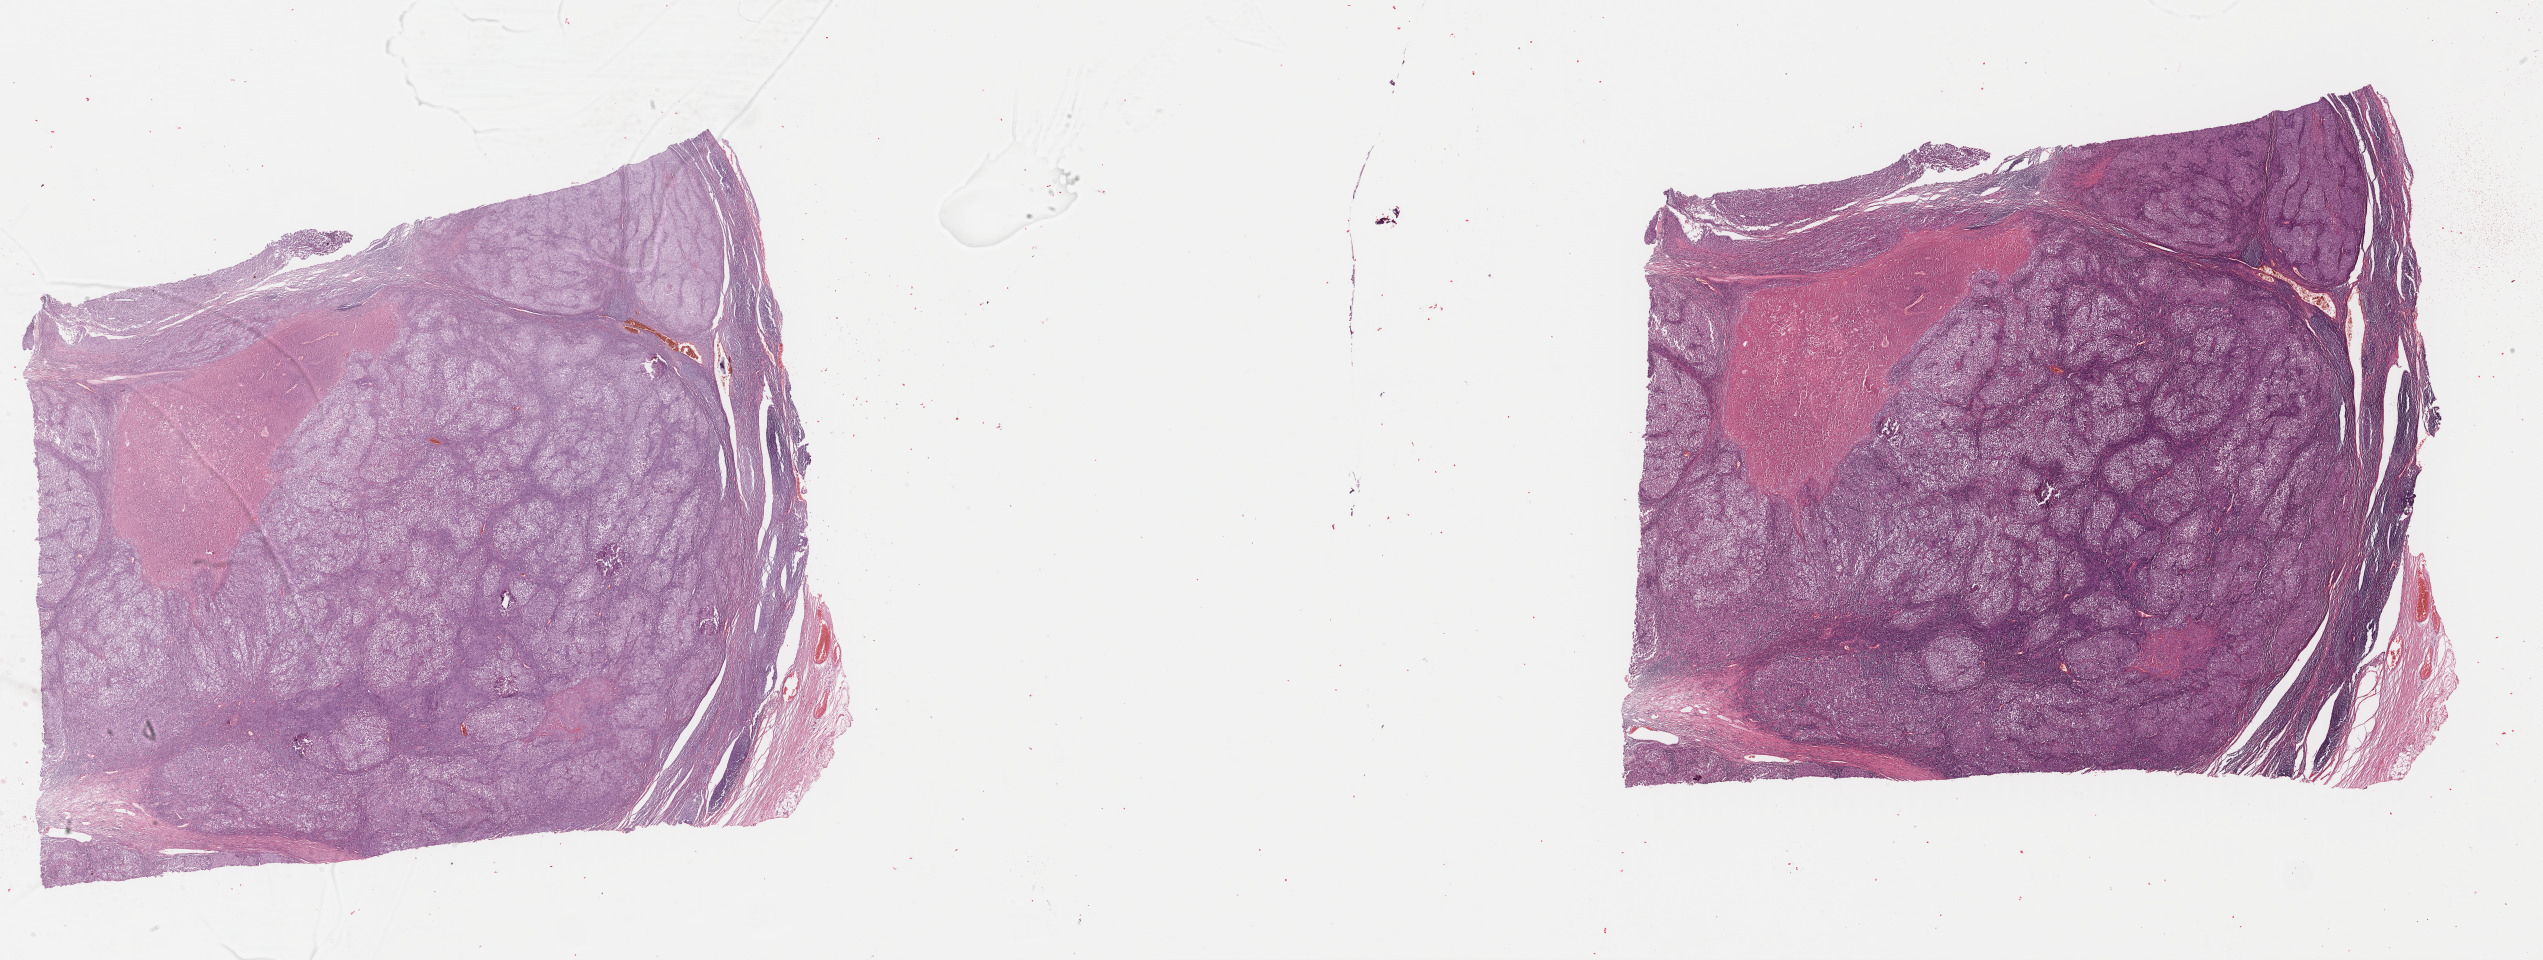
H&E-stained whole-slide image, shown as a low-resolution overview of the whole scanned area (about 40.0 x 15.1 mm, from a 40x scan), FFPE section, metastatic tumour sample, sampled site: lymph node. Male, age 65 years at initial diagnosis.
This section: metastatic tumour tissue. Patient diagnosis: Malignant melanoma, NOS.